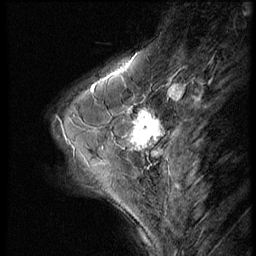
Breast MRI (dynamic contrast-enhanced), one sagittal slice; slice 18 of 56 in the series (ordered by position); dynamic contrast-enhanced series, image 2 of 3 at this slice position (ordered by acquisition); 1.5 T; TE 4.2 ms, TR 9 ms; 2.5 mm slice thickness; 256 × 256 image matrix. Patient: female, 46 years. From the clinical record (not read from this slice): setting: breast cancer imaged before/during neoadjuvant chemotherapy; receptor status: HER2-positive.
Annotated regions visible in this slice (semi-automatic segmentation, software-assisted and operator-edited):
- analysis volume of interest (the breast-tissue region the enhancement analysis was run in; not a lesion): box from (x=64, y=98) to (x=174, y=182) px
- tumour enhancement mask (voxels above the 140 % enhancement threshold inside the analysis volume of interest): (x=131, y=109)–(x=161, y=148)